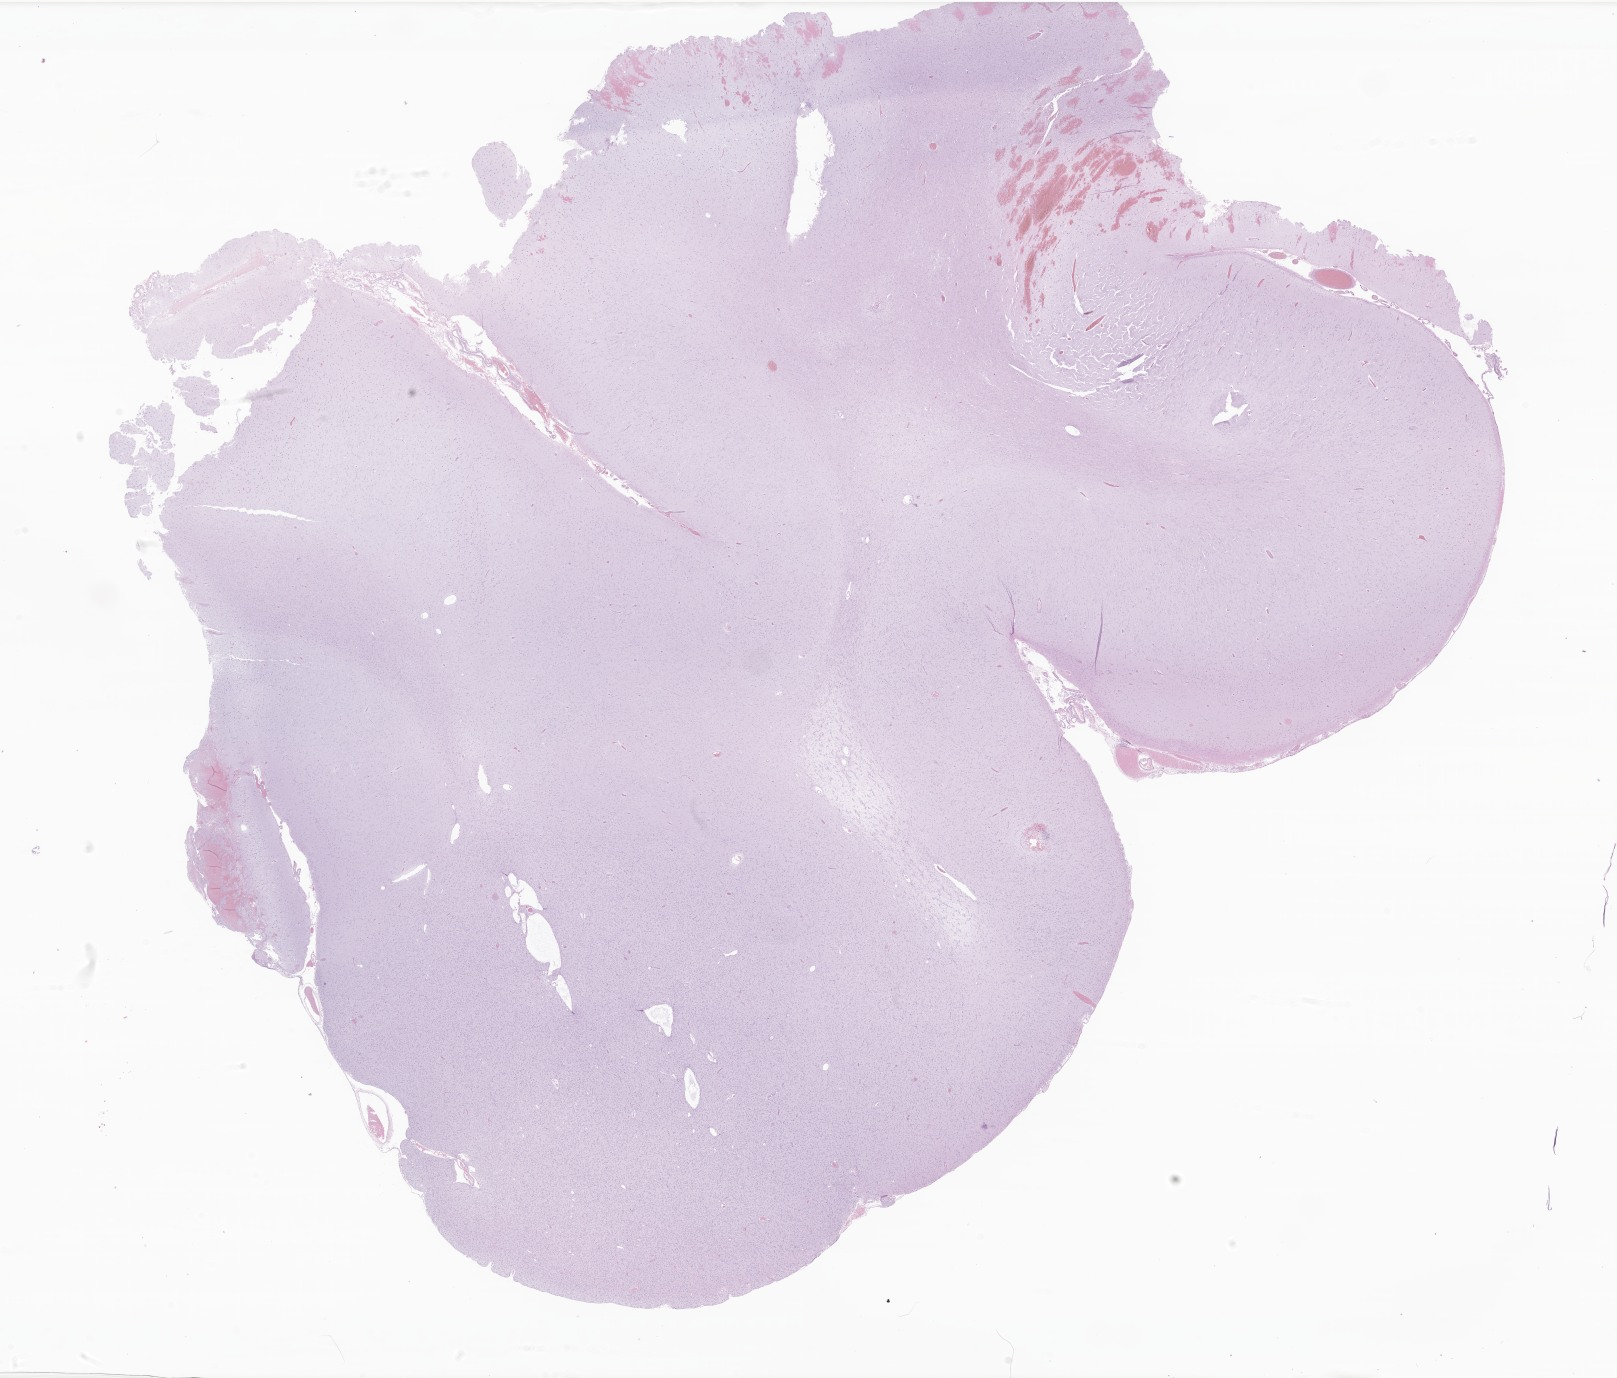
H&E whole-slide image of tumor tissue from the temporal lobe — a low-resolution overview of the entire scanned area, about 27.3 x 23.2 mm, FFPE section. Patient: female, age 176 months (14 years 8 months).
- diagnosis (ICD-O-3 morphology term): Ganglioglioma, NOS